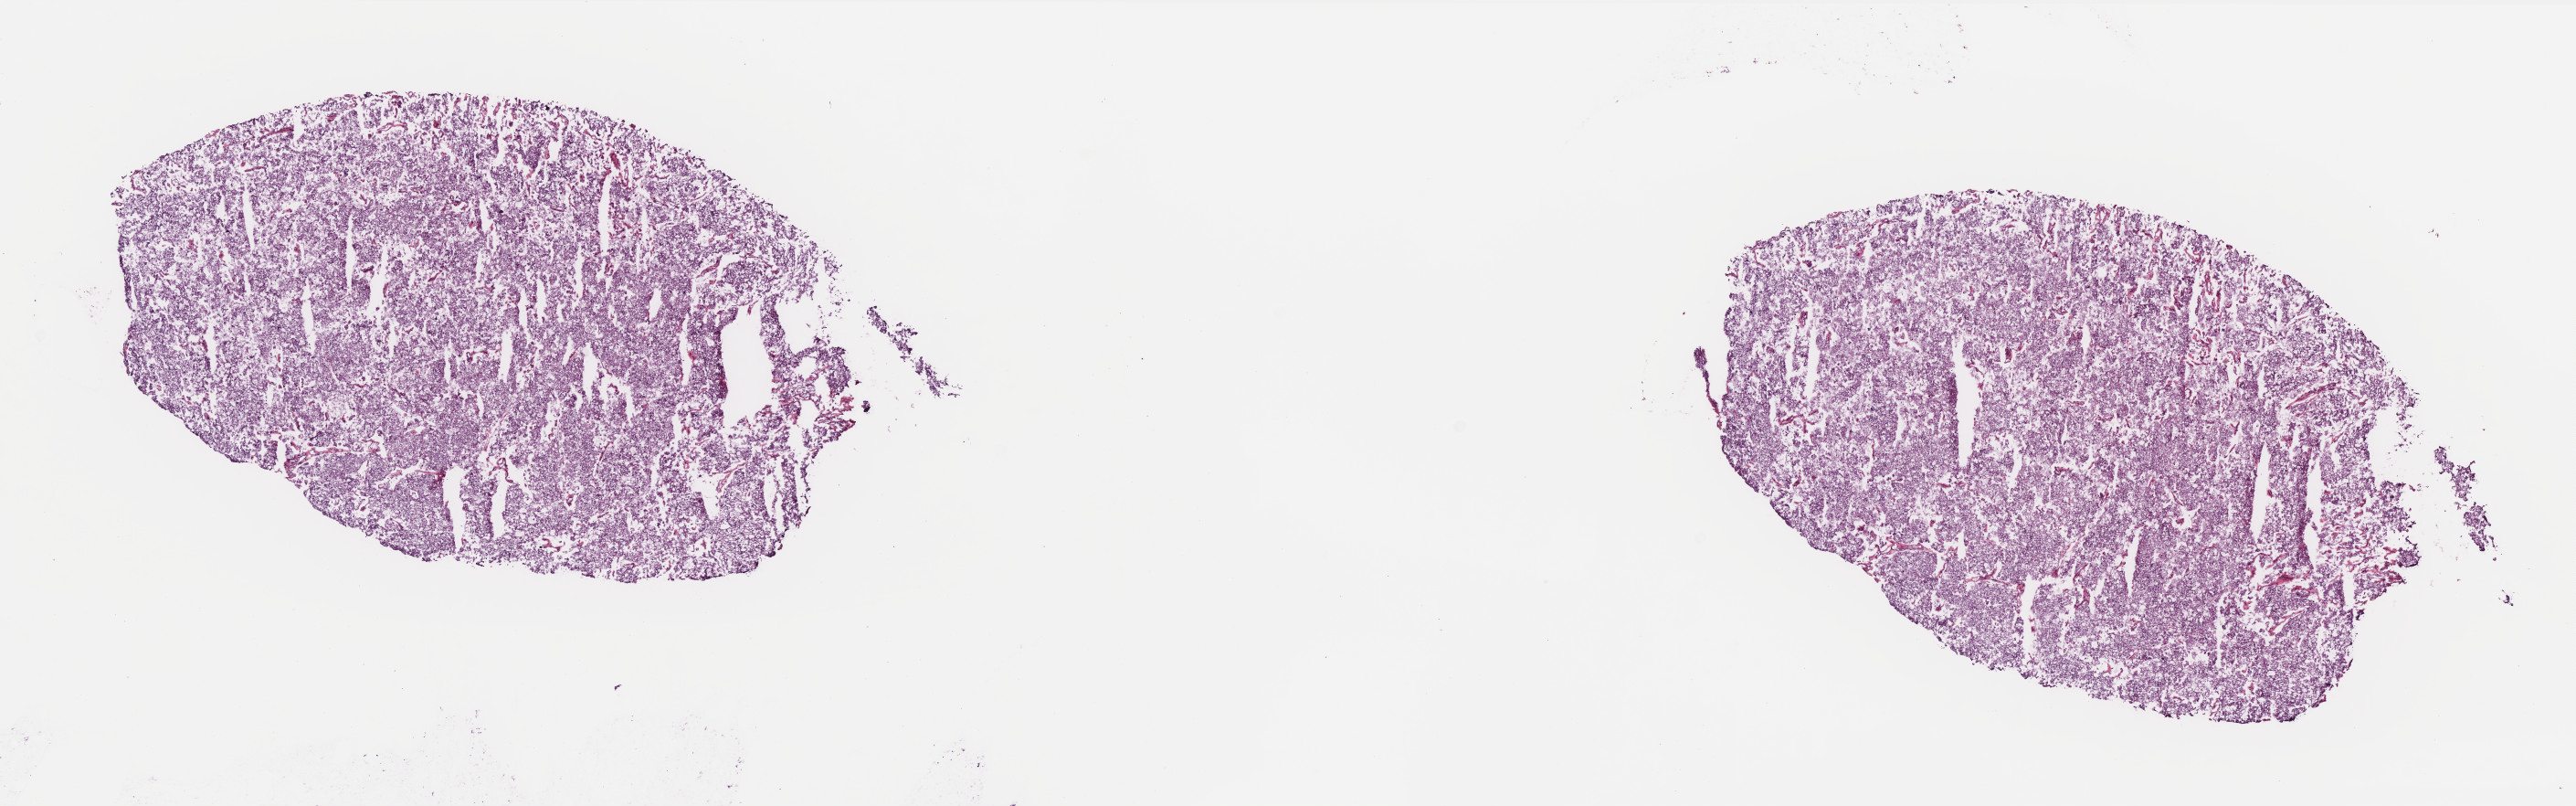
H&E whole-slide image, shown as a low-resolution overview of the whole scanned area (about 22.6 x 7.1 mm, acquisition: 40x scan). Frozen section from the top of the tissue portion. Kidney, primary tumour sample. Male patient; age at initial diagnosis 45 years. Pathologist review of this section (percent, as recorded): tumour cells 90%, tumour nuclei 95%, normal cells 0%, stromal cells 0%, necrosis 10%. Infiltration values recorded for this section: lymphocyte infiltration 0%, monocyte infiltration 0%, neutrophil infiltration 0%.
Laterality: left. Diagnosis: Renal cell carcinoma, chromophobe type. AJCC pathologic stage: I (7th edition).